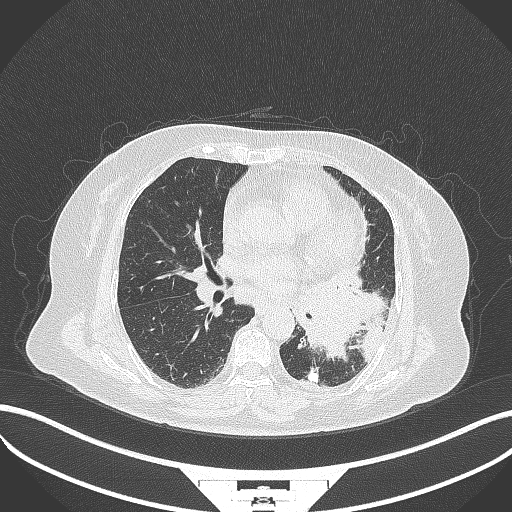
Chest CT, one axial slice; slice 171 of 322 in the series (ordered by position); reconstruction kernel B70f; lung window (W 1500 / L -600 HU); 1 mm slice thickness; 512 × 512 image matrix, field of view 400 × 400 mm. Patient: female, 69 years. Case-level facts recorded for this patient, not image findings: clinical TNM (as recorded): T2b N3 M1.
Structures marked on this image (rectangle marked by the reading radiologist):
- lung tumour (recorded histology: adenocarcinoma): bounding box (x1, y1, x2, y2) in pixels: (293, 273, 385, 360)